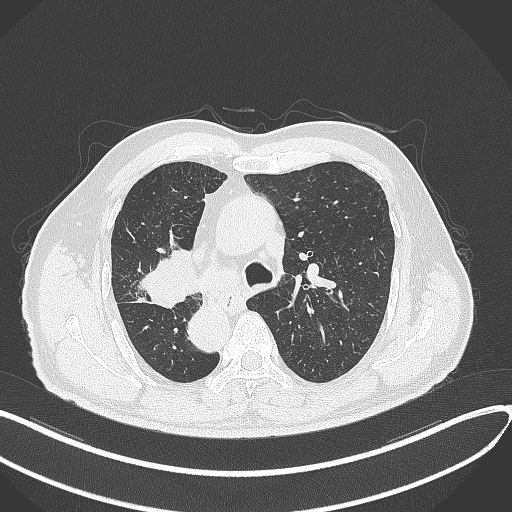
Chest CT, one axial slice; slice 207 of 300 in the series (ordered by position); 120 kVp; lung window (W 1500 / L -600 HU); 1 mm slice thickness; 512 × 512 image matrix. Male patient, age 67 years. From the clinical record (not read from this slice): clinical TNM (as recorded): T2a N0 M0.
Outlined on this slice (bounding box drawn by a radiologist):
- lung tumour (recorded histology: squamous cell carcinoma): bounding box [x1, y1, x2, y2] px = [136, 244, 201, 309]